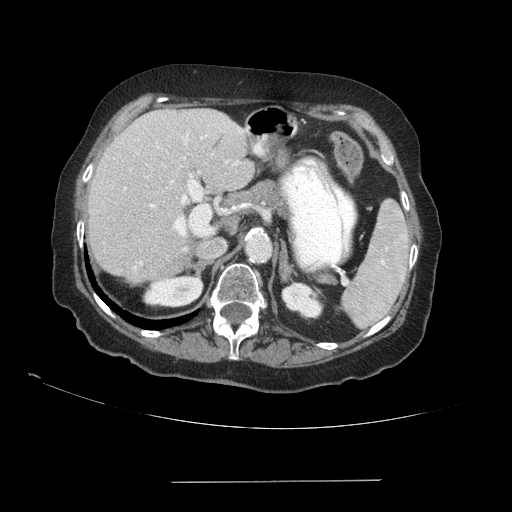
Contrast-enhanced abdominal CT (liver protocol), one axial slice; position 59 of 89 along the scan axis; reconstruction kernel STANDARD; 140 kVp; soft-tissue window (W 400 / L 40 HU); 2.5 mm slice thickness; 512 × 512 image matrix, field of view 400 × 400 mm. Case-level facts recorded for this patient, not image findings: diagnosis: hepatocellular carcinoma (patient treated with transarterial chemoembolisation; whether this scan precedes or follows treatment is not stated here); TNM stage (as recorded): Stage-IVA; Child-Pugh class: A; tumour differentiation: poorly differentiated.
Structures marked on this image (semi-automatically segmented with operator editing):
- liver parenchyma outside the tumour (the mass and vessels are separate outlines, so this box may not span the whole liver): box from (x=88, y=108) to (x=254, y=284) px
- liver vessels: (x=124, y=129)–(x=243, y=270)